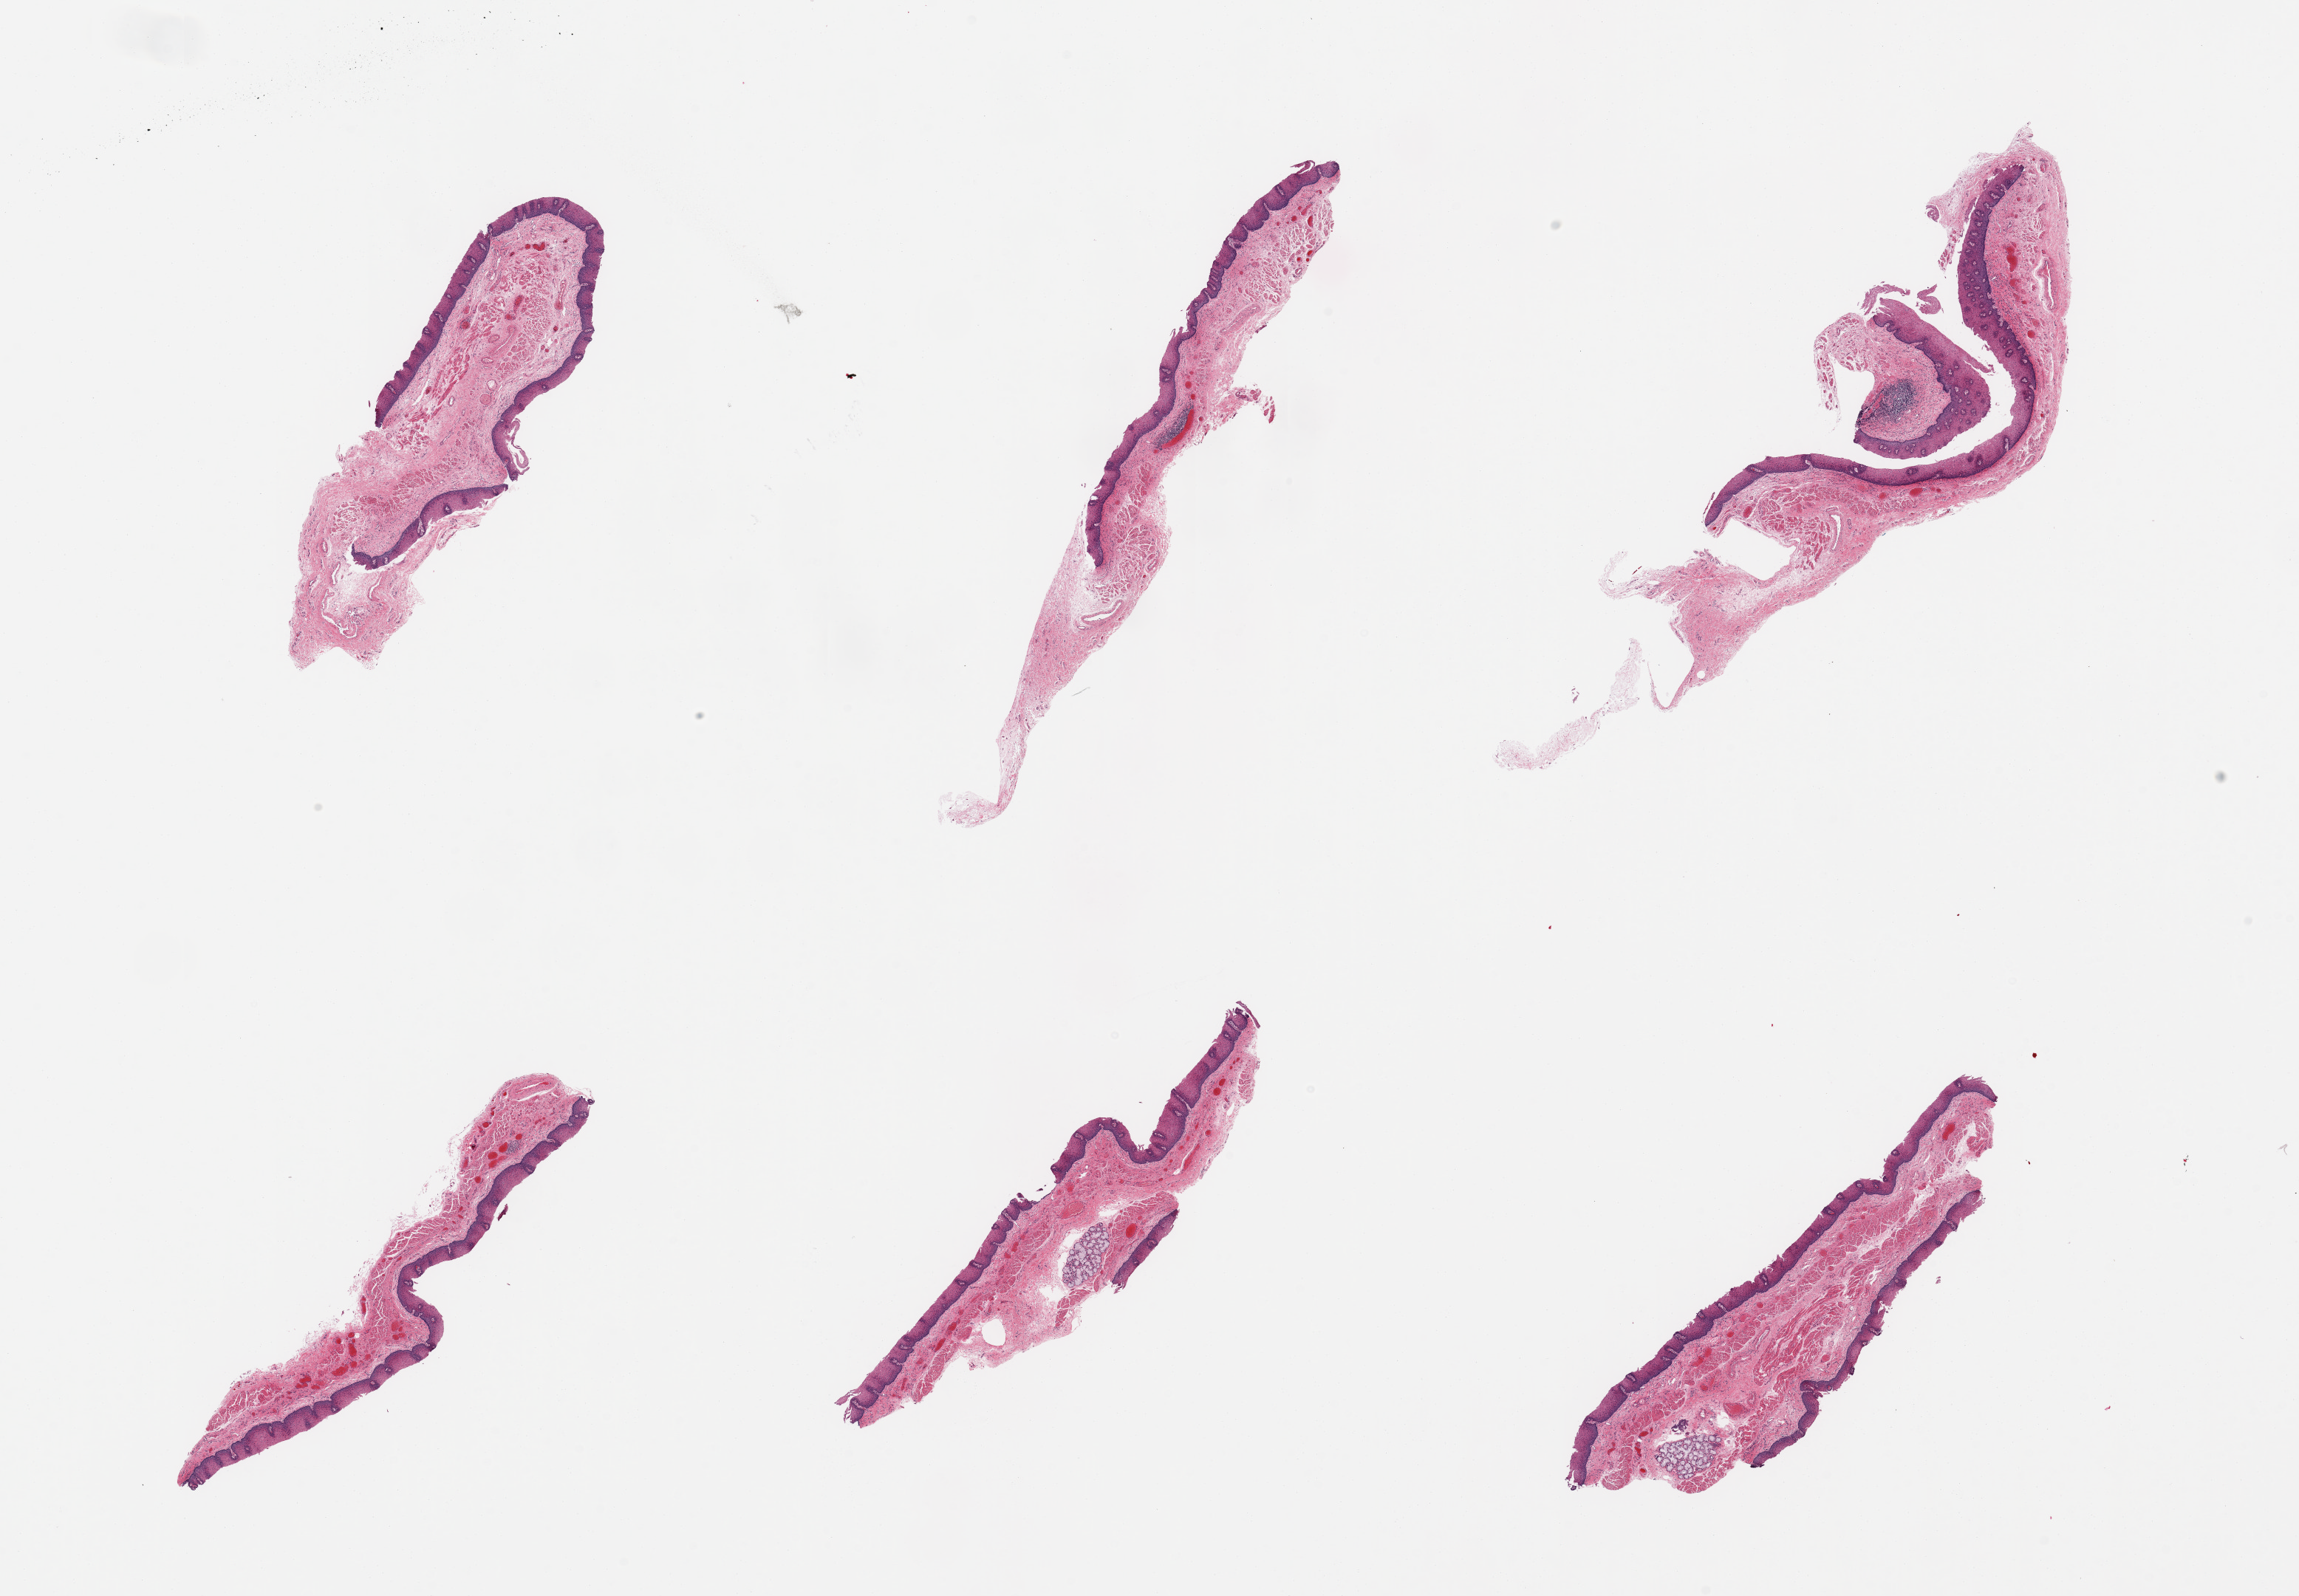
Whole-slide image, hematoxylin and eosin (H&E) stain, shown as a low-resolution overview of the whole scanned area (about 24.6 x 17.1 mm, slide scanned at 20x), PAXgene-fixed paraffin-embedded (PFPE) section, target tissue: esophageal mucous membrane, tissue donor sample. Male donor.
* pathologist's review note for this sample: 6 pieces; well dissected